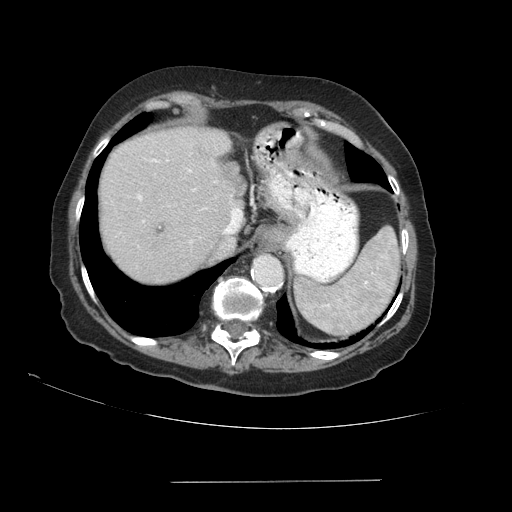
Contrast-enhanced abdominal CT (liver protocol), one axial slice. Position 72 of 89 along the scan axis. 140 kVp. Soft-tissue window (W 400 / L 40 HU). 2.5 mm slice thickness. 512 × 512 image matrix, field of view 400 × 400 mm. Case-level facts recorded for this patient, not image findings: diagnosis: hepatocellular carcinoma (patient treated with transarterial chemoembolisation; whether this scan precedes or follows treatment is not stated here); TNM stage (as recorded): Stage-IVA; Child-Pugh class: A; tumour differentiation: poorly differentiated.
Outlined on this slice (semi-automatically segmented with operator editing):
- abdominal aorta: bounding box <253,256,280,285> (left, top, right, bottom; pixels)
- liver parenchyma outside the tumour (the mass and vessels are separate outlines, so this box may not span the whole liver): <100,126,244,282>
- liver vessels: <137,159,242,242>